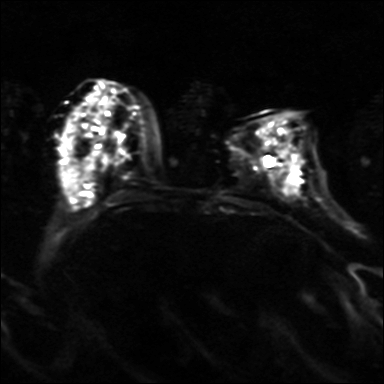
Breast MRI, one axial slice; position 13 of 36 along the scan axis; diffusion-weighted series; image 2 of 4 stored at this slice position (different b-values; order by instance number); 3 T; 4 mm slice thickness; 384 × 384 image matrix, field of view 320 × 320 mm. Female patient.
Annotated regions visible in this slice (outlined manually by an expert reader):
- tumour on diffusion-weighted imaging: bounding box <280,150,298,191> (left, top, right, bottom; pixels)